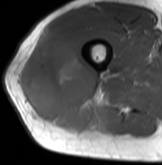
MRI of an extremity soft-tissue mass, one axial slice; position 45 of 61 along the scan axis; MR volume resampled by the dataset authors to the PET/CT grid (not the native acquisition matrix); 3.27 mm slice thickness; 162 × 165 image matrix, field of view 158 × 161 mm. Male patient. Case-level facts recorded for this patient, not image findings: histological type: poorly differentiated synovial sarcoma; grade: high; site of the primary tumour: right buttock.
Structures marked on this image (expert contour drawn on MRI and transferred to this co-registered scan by the dataset authors):
- gross tumour volume including surrounding oedema: bounding box <22,31,108,130> (left, top, right, bottom; pixels)
- gross tumour volume (mass): <22,31,104,130>